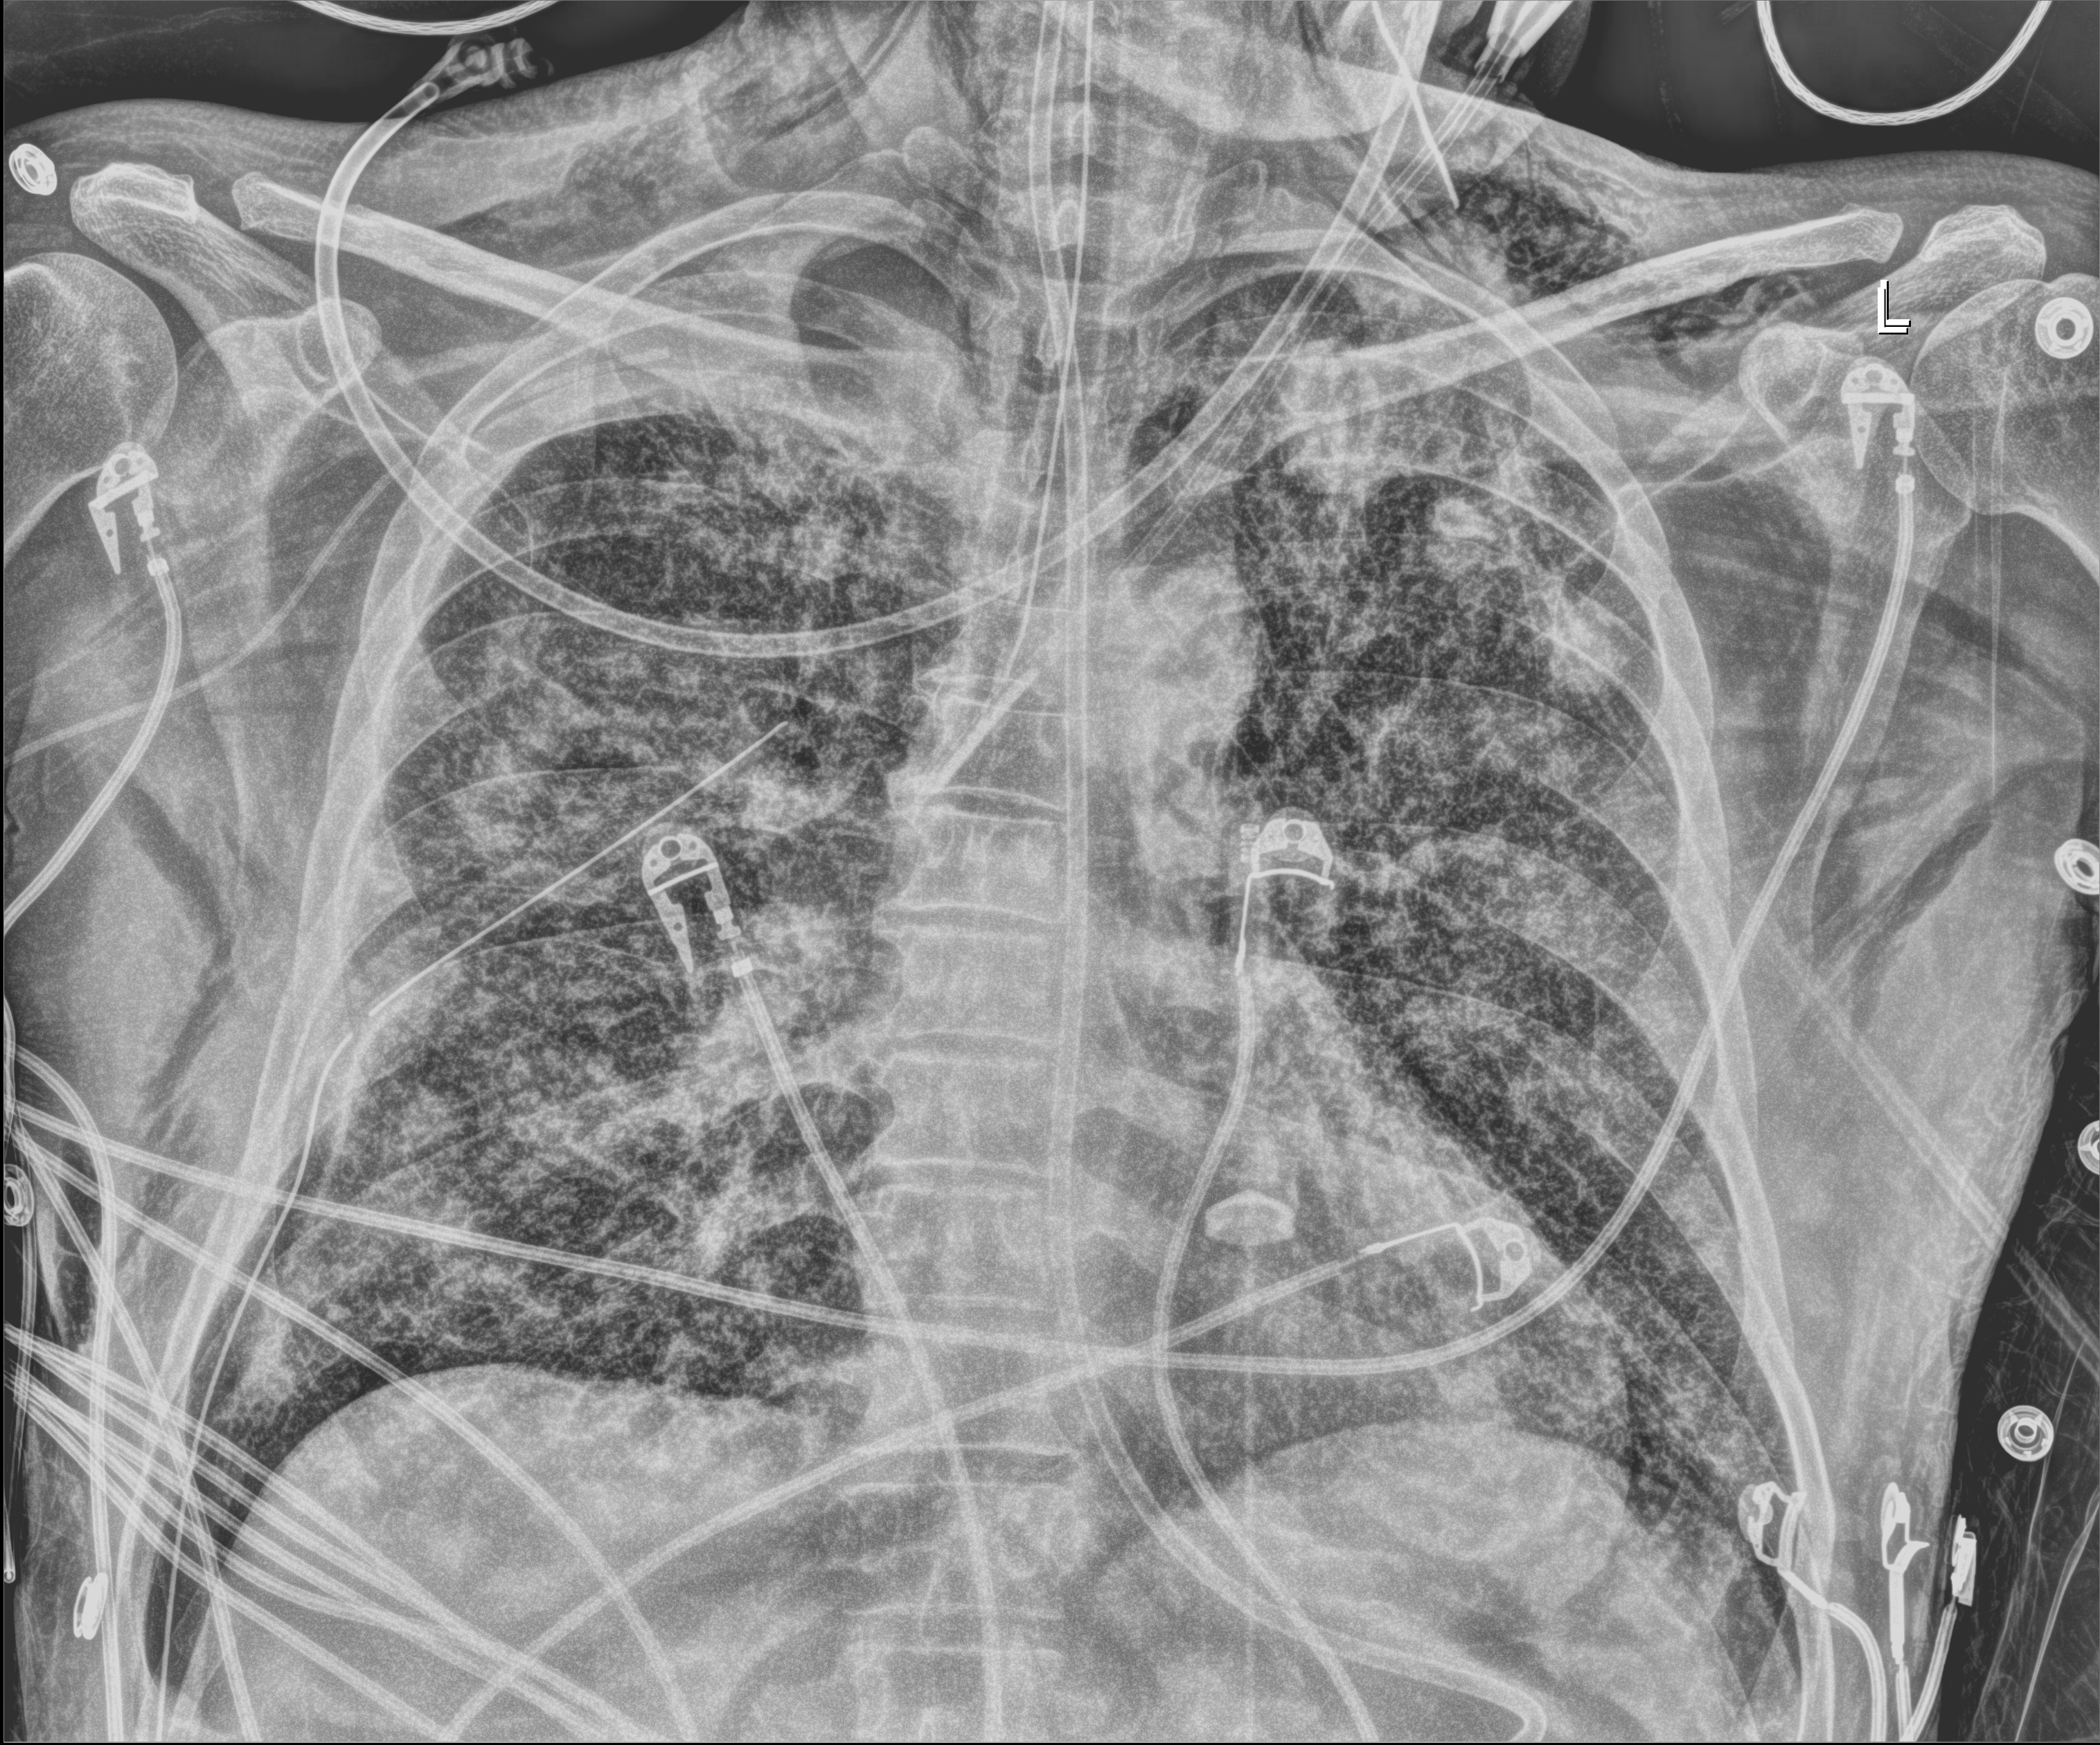
Portable chest radiograph. Male patient hospitalised with COVID-19, age 18–59 years.
Admission-level facts for this patient (not findings on this image; timing relative to this image not recorded): admitted to intensive care during this hospital stay: yes; length of hospital stay: 42 days.